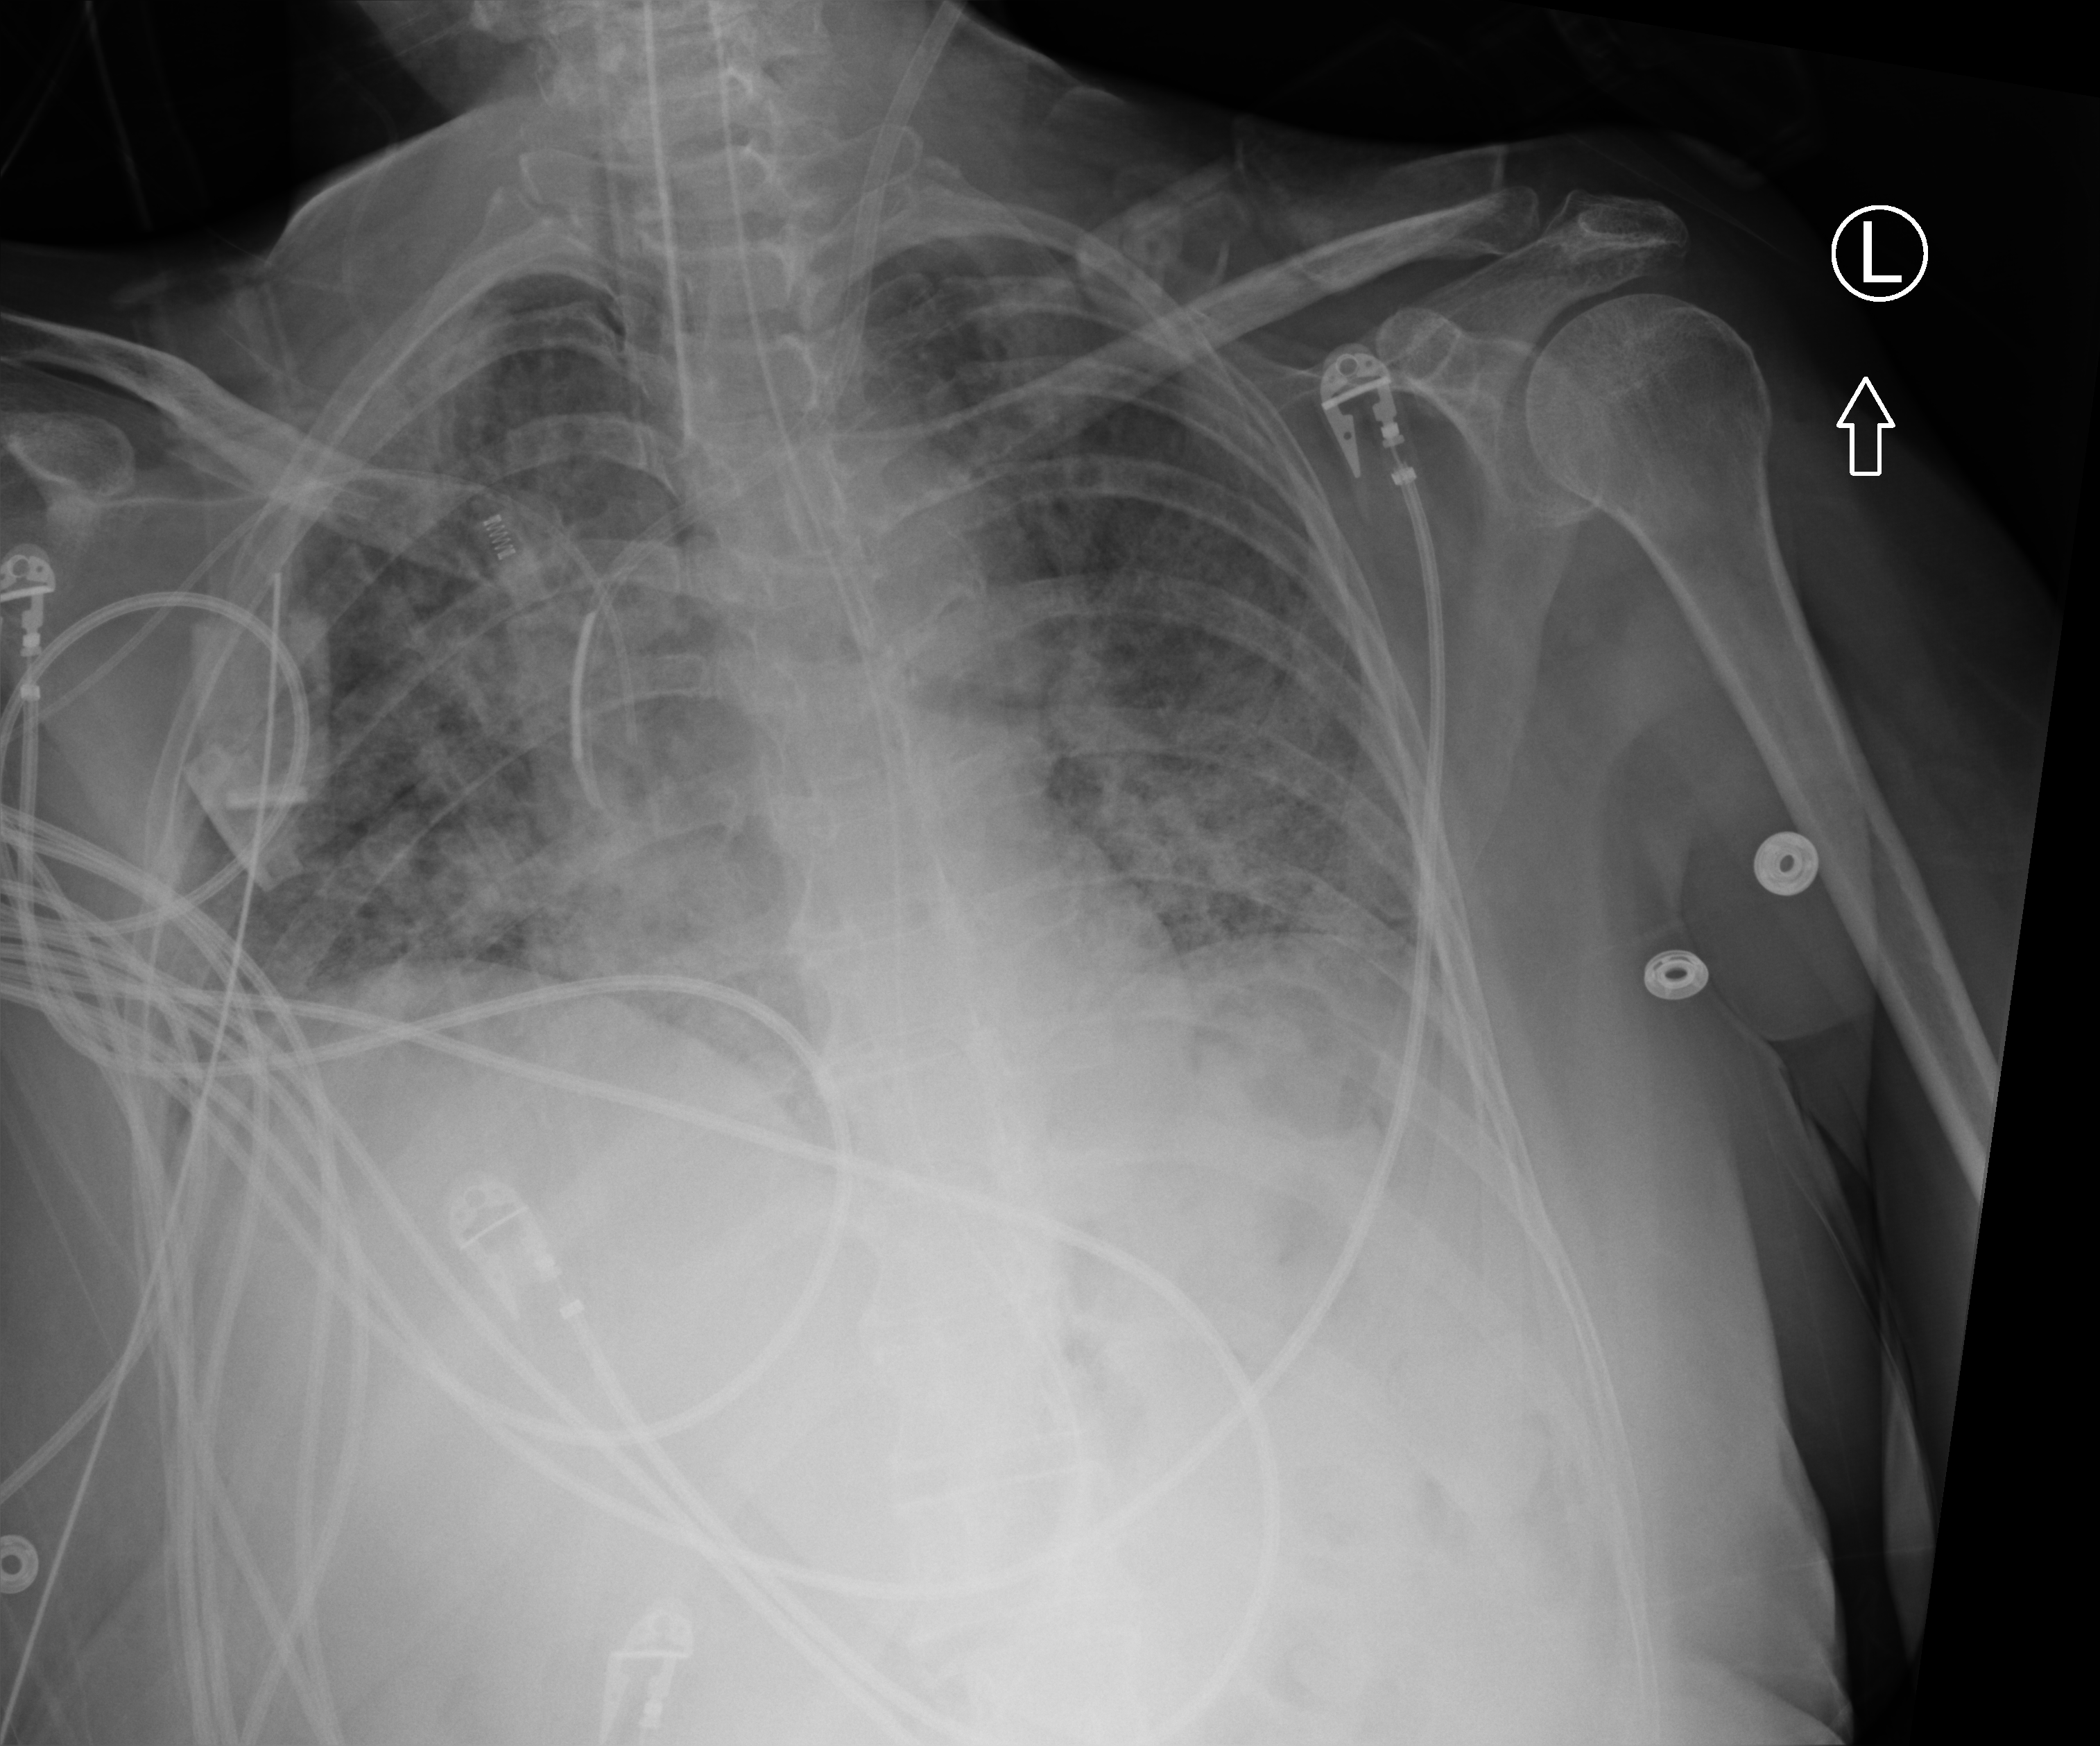
Portable chest radiograph; anteroposterior (AP) projection. Patient hospitalised with COVID-19; female, aged 60–74 years.
From the hospital-stay record, not from the radiograph (when in the stay this image was taken is not recorded):
- other chronic lung disease (admission record): no